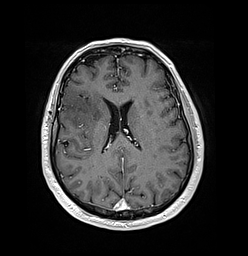
Brain MRI from a brain-tumour surgery series, one axial slice; position 66 of 176 along the scan axis; T1-weighted post-contrast; 248 × 256 image matrix, field of view 242 × 250 mm. Case-level facts recorded for this patient, not image findings: histopathology: Oligodendroglioma; WHO grade: 3; IDH mutation: yes; tumour location: Right Frontal.
Outlined on this slice (outlined manually by an expert reader):
- tumour: bounding box <76,118,81,122> (left, top, right, bottom; pixels)